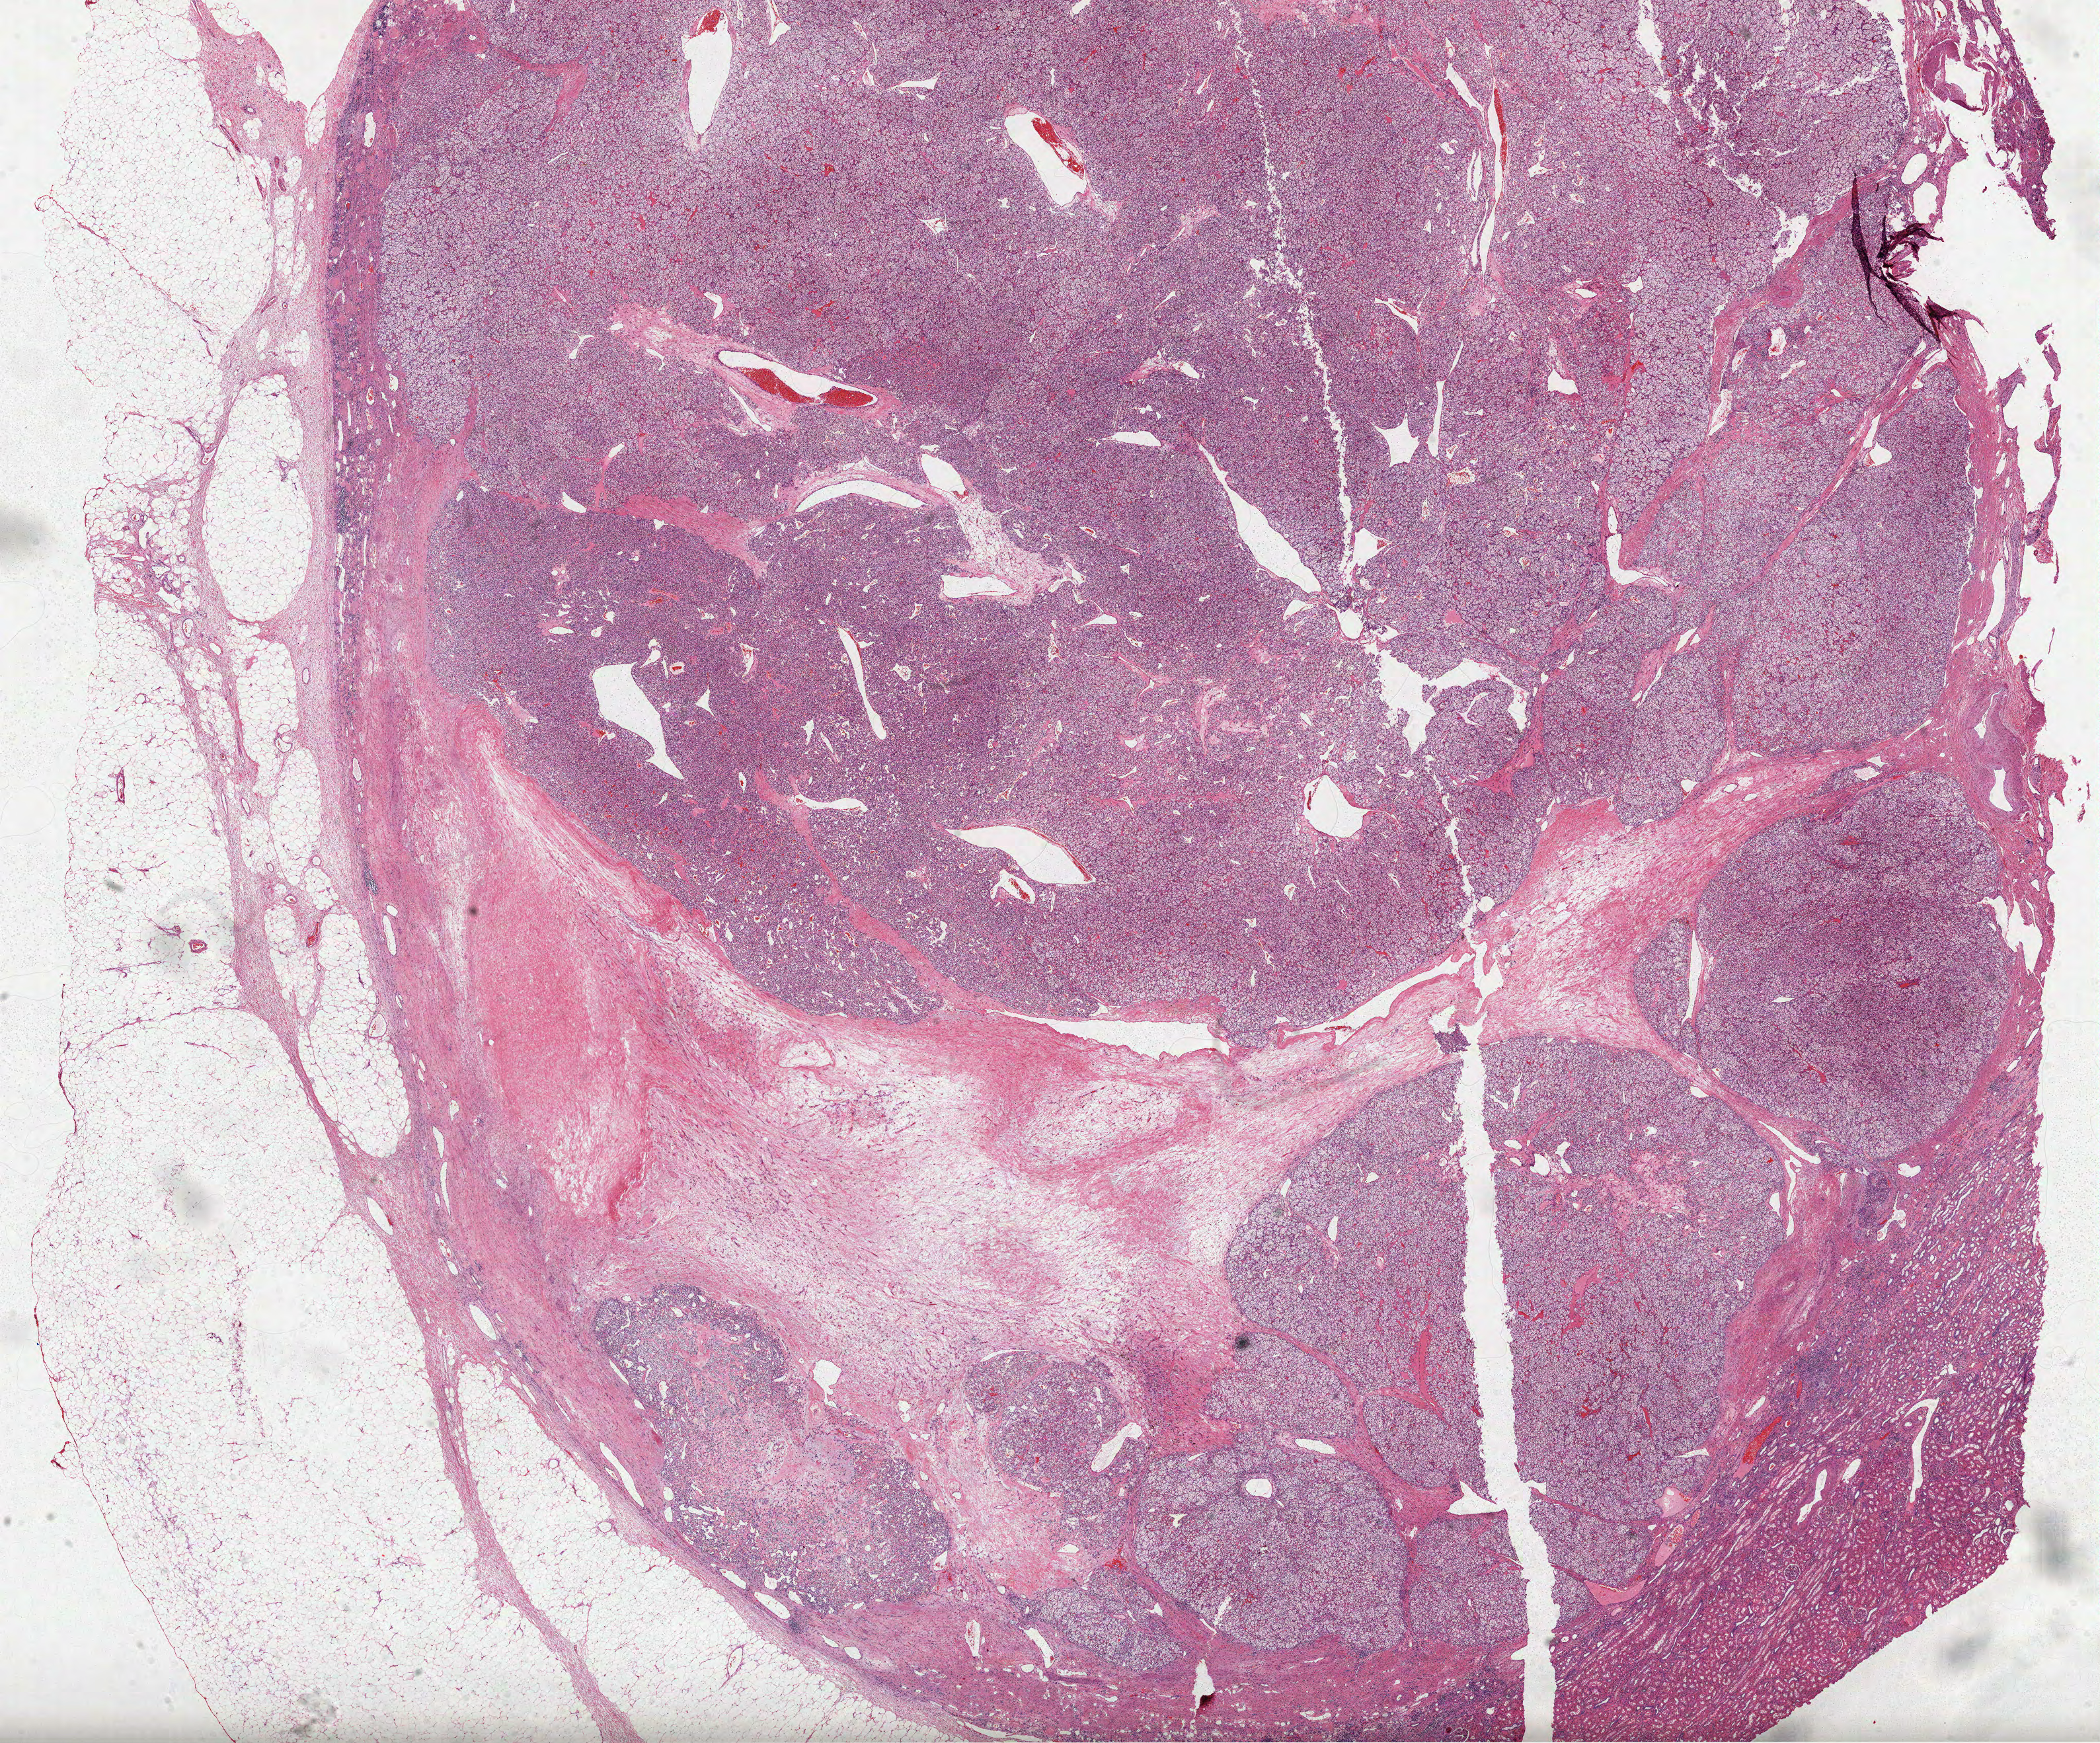
Digitized H&E tissue section (whole slide), shown as a low-resolution overview of the whole scanned area (about 25.6 x 21.3 mm, acquisition: 40x scan). Formalin-fixed paraffin-embedded (FFPE) diagnostic section. Primary tumour sample from the kidney. Patient: female, age at initial diagnosis 66 years. Histologic grade: G3 (poorly differentiated).
- pathologic diagnosis: Clear cell adenocarcinoma, NOS
- AJCC pathologic stage: I